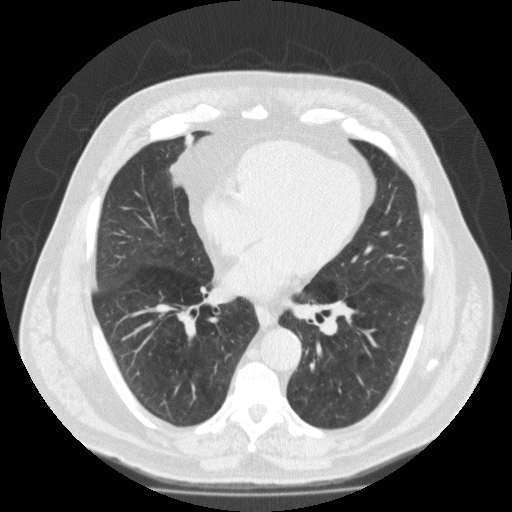
Low-dose screening chest CT, one axial slice. Slice 89 of 188 in the series (ordered by position). Reconstruction kernel FC10. 120 kVp. Lung window (W 1500 / L -600 HU). 2 mm slice thickness. 512 × 512 image matrix.
Outlined on this slice (expert manual segmentation):
- lesion 1 (tumor, lower lobe of right lung): box from (x=169, y=133) to (x=197, y=185) px